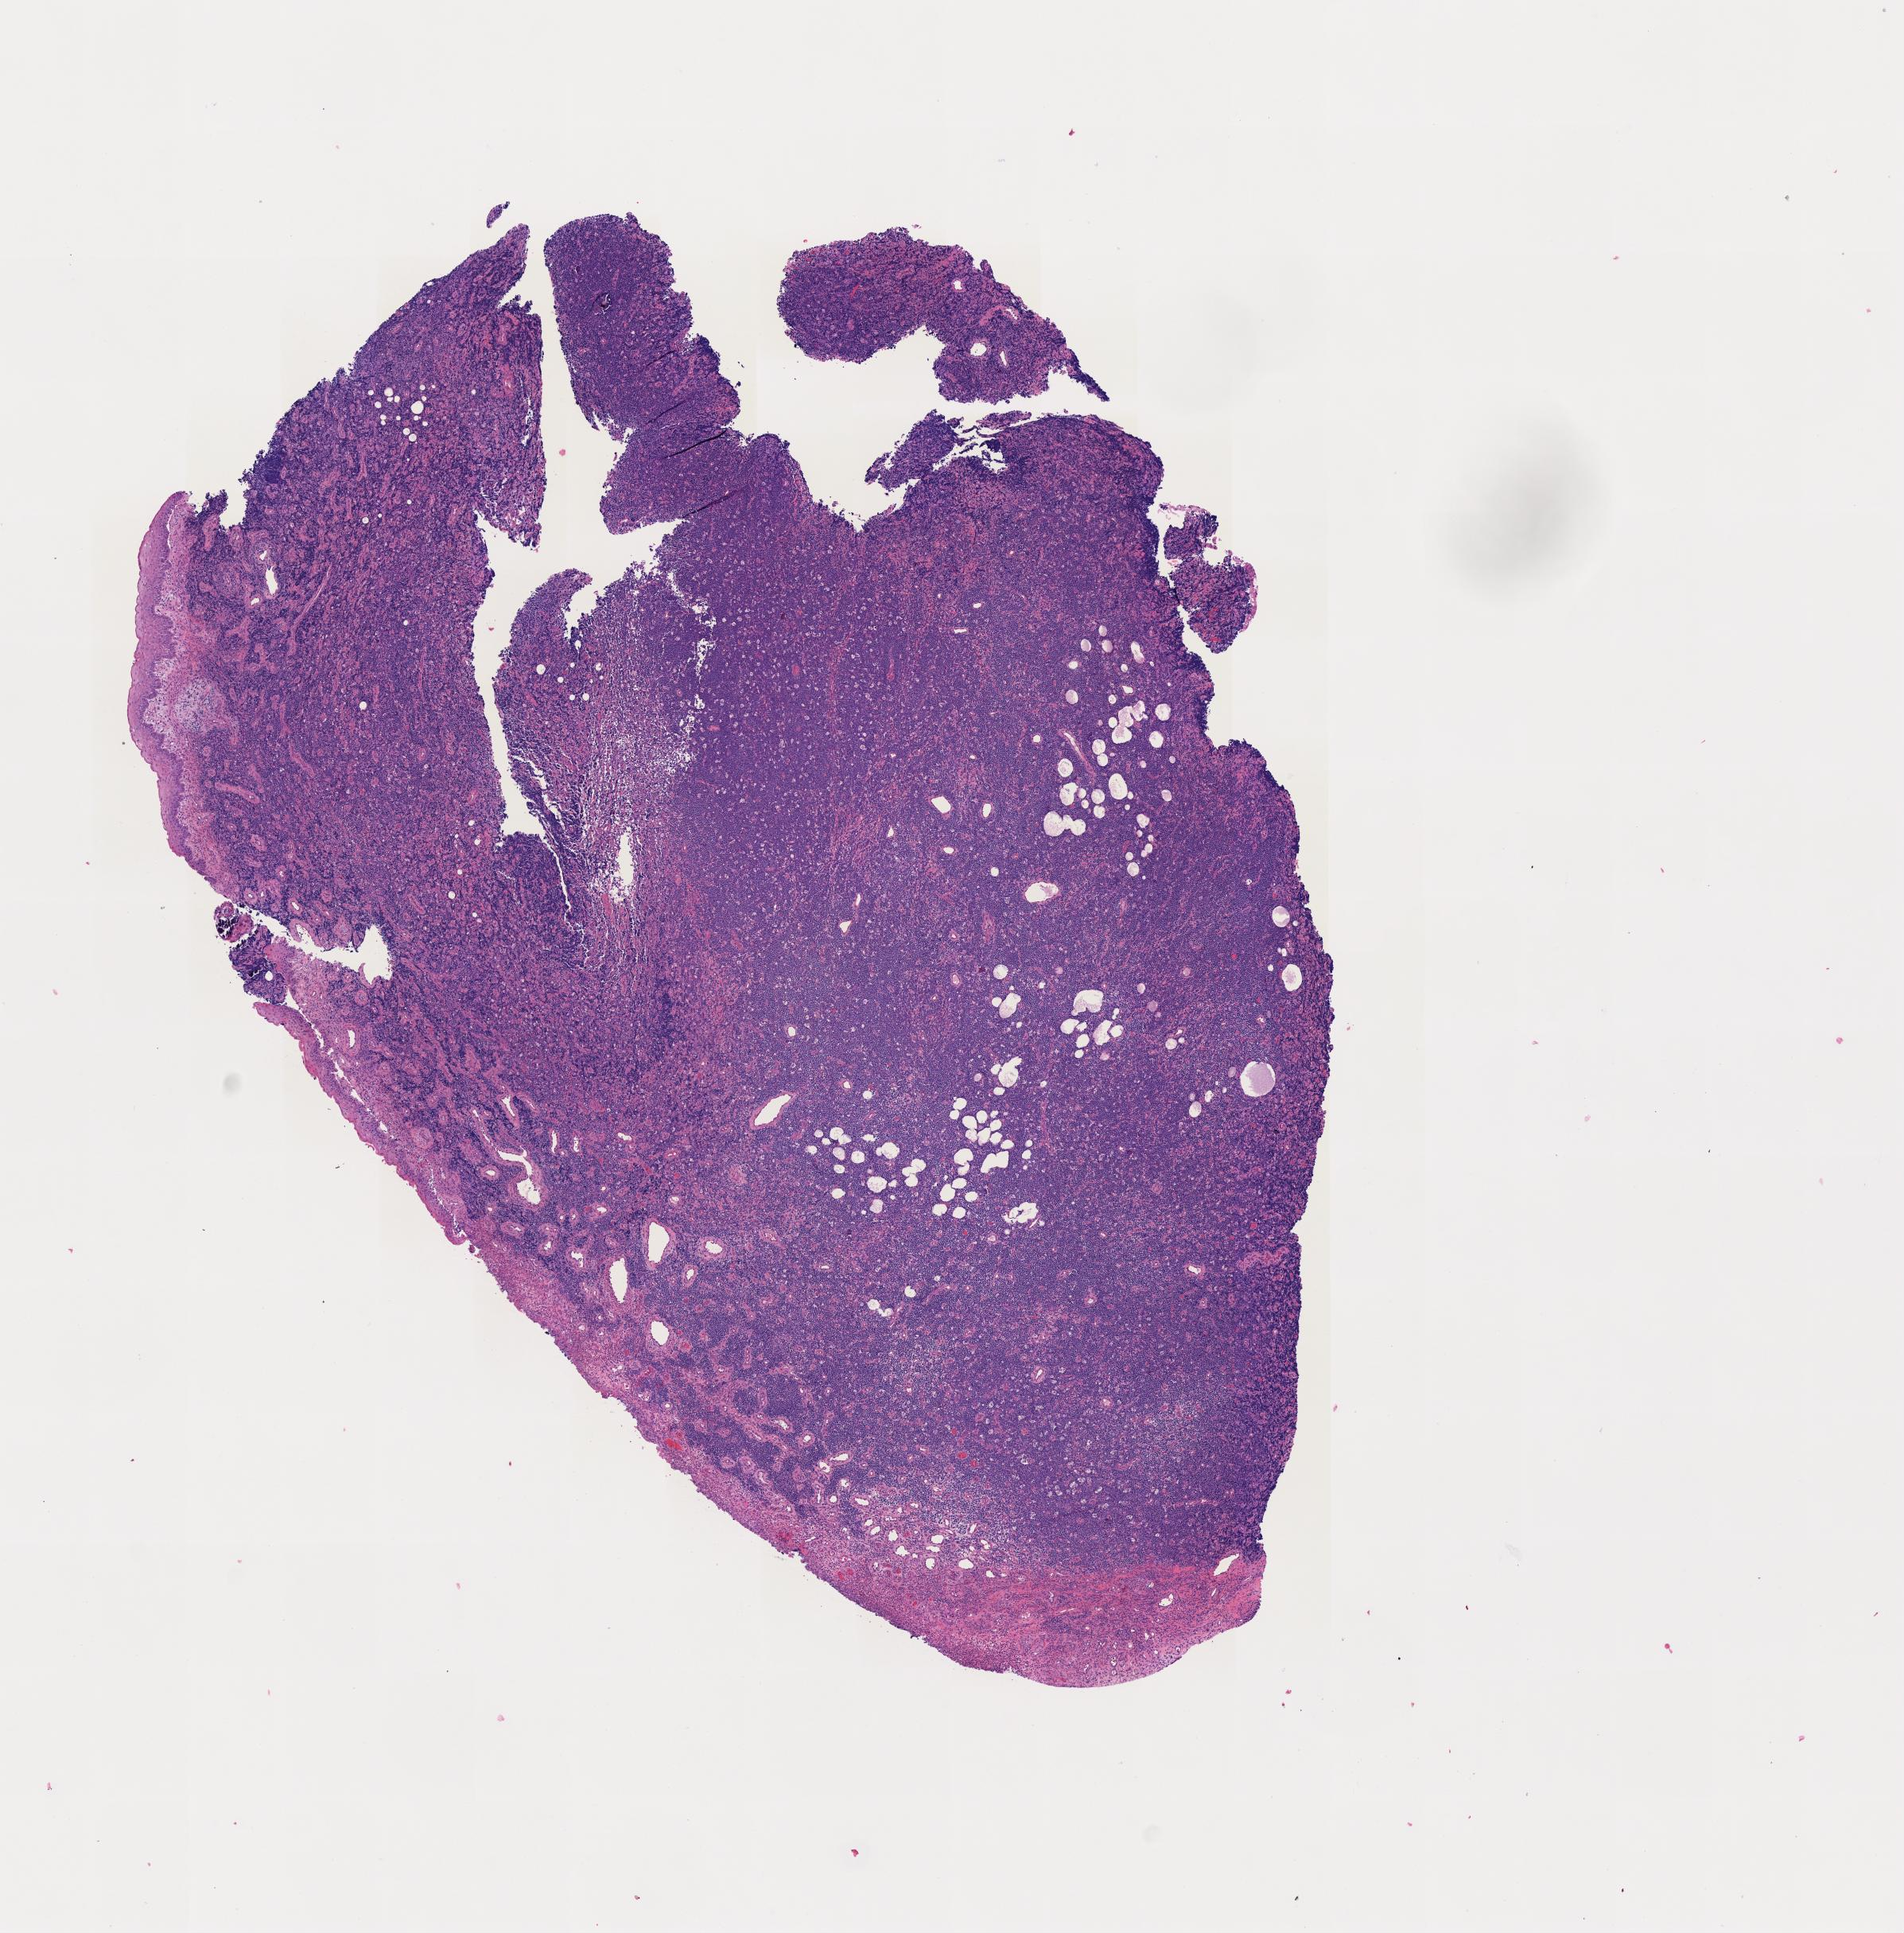
Haematoxylin and eosin whole-slide image — low-resolution overview of the scanned area, specimen: tumor tissue, anatomic site: mandible. Patient: male, age 11 years.
* histologic diagnosis: Burkitt lymphoma, NOS